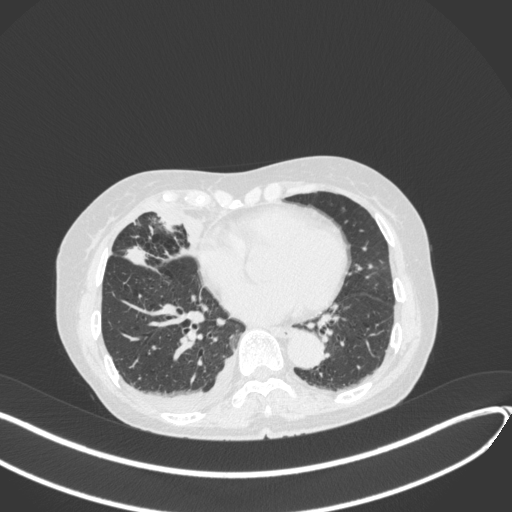
Chest CT, one axial slice. Position 154 of 418 along the scan axis. Lung window (W 1500 / L -600 HU). 512 × 512 image matrix, field of view 400 × 400 mm. Patient: female, 75 years. Case-level facts recorded for this patient, not image findings: clinical TNM (as recorded): T2a N3 M0.
Structures marked on this image (bounding box drawn by a radiologist):
- lung tumour (recorded histology: adenocarcinoma): bounding box (x1, y1, x2, y2) in pixels: (119, 242, 152, 270)